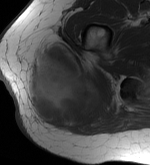
MRI of an extremity soft-tissue mass, one axial slice; position 20 of 56 along the scan axis; MR volume resampled by the dataset authors to the PET/CT grid (not the native acquisition matrix); 150 × 165 image matrix. Female patient. From the clinical record (not read from this slice): histological type: epithelioid sarcoma with vascular differentiation; site of the primary tumour: right buttock.
Outlined on this slice (expert contour drawn on MRI and transferred to this co-registered scan by the dataset authors):
- gross tumour volume (mass): bounding box <25,42,111,130> (left, top, right, bottom; pixels)